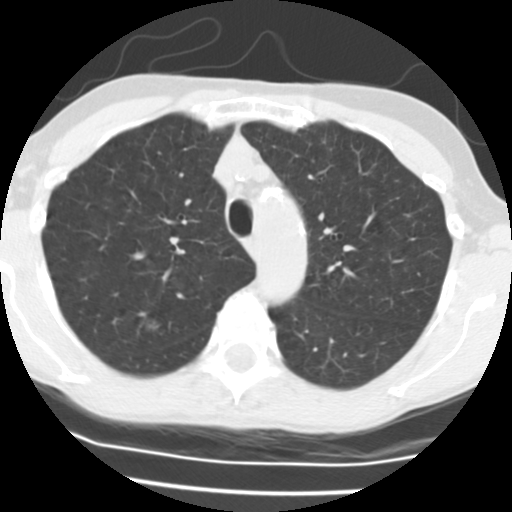
Axial slice from a low-dose chest CT screening exam, third annual screen, lung window (W 1500 / L -600 HU), standard (soft-tissue) reconstruction kernel (STANDARD), 120 kVp, slice 161 of 195 in the series, 512 × 512 image matrix, field of view 275 × 275 mm. Female participant, aged 58 years at enrolment. Current smoker at enrolment.
Expert-annotated lung lesion, bounding box [x1, y1, x2, y2] px = [133, 310, 166, 340]. The screening reader recorded 3 non-calcified nodules or masses ≥4 mm on this exam (right upper lobe, left upper lobe, right upper lobe); which of them this box marks is not recorded. Official screen result: positive, other. Lung cancer was diagnosed 153 days after this screen: bronchiolo-alveolar adenocarcinoma, NOS, right upper lobe, well differentiated (G1), stage IA (AJCC 6th edition), 8 mm at pathology.